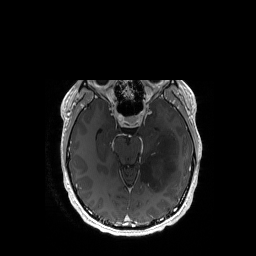
Brain MRI from a brain-tumour surgery series, one axial slice; slice 108 of 192 in the series (ordered by position); T1-weighted post-contrast; 1 mm slice thickness; 256 × 256 image matrix, field of view 256 × 256 mm. Case-level facts recorded for this patient, not image findings: histopathology: Astrocytoma; WHO grade: 3; IDH mutation: yes; tumour location: Left Temporal.
Structures marked on this image (expert manual segmentation):
- tumour: bounding box <140,131,178,191> (left, top, right, bottom; pixels)